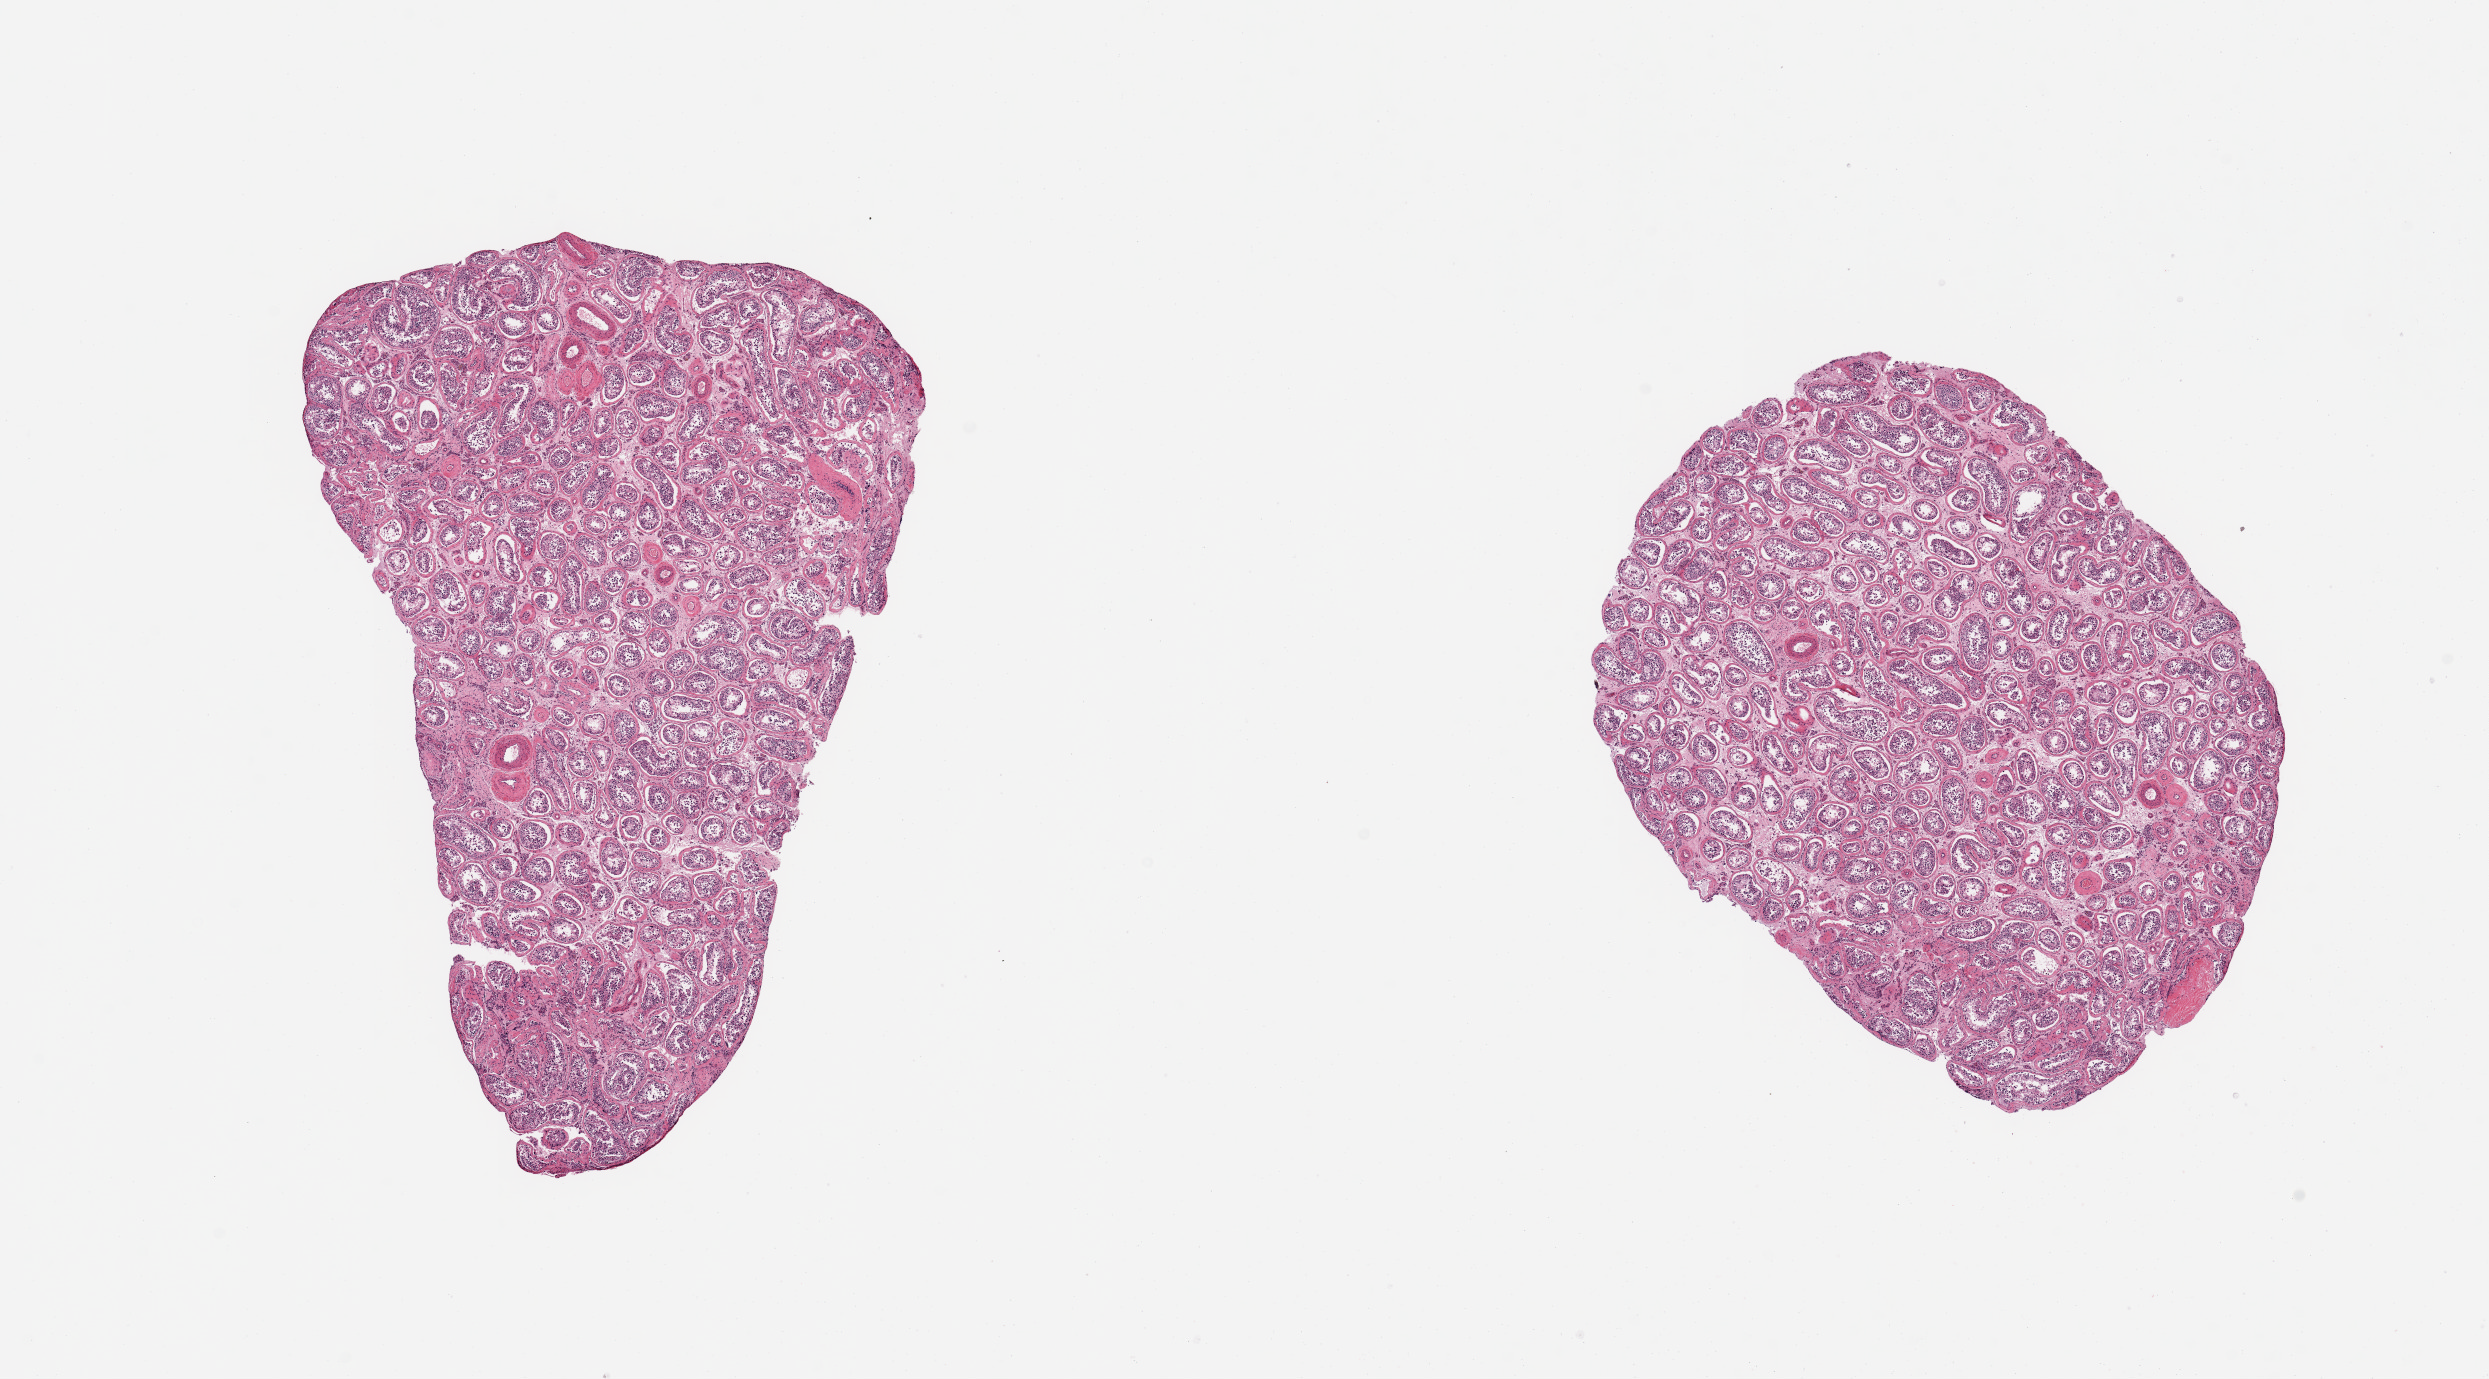
Whole-slide image, haematoxylin and eosin stain — a low-resolution overview of the entire scanned area, about 19.7 x 10.9 mm (acquisition: 20x scan). PAXgene-fixed paraffin-embedded (PFPE) section. Section of testis (target tissue). Donor tissue sample. Donor sex: male.
- review note (as recorded): 2 pieces; spermatogenesis